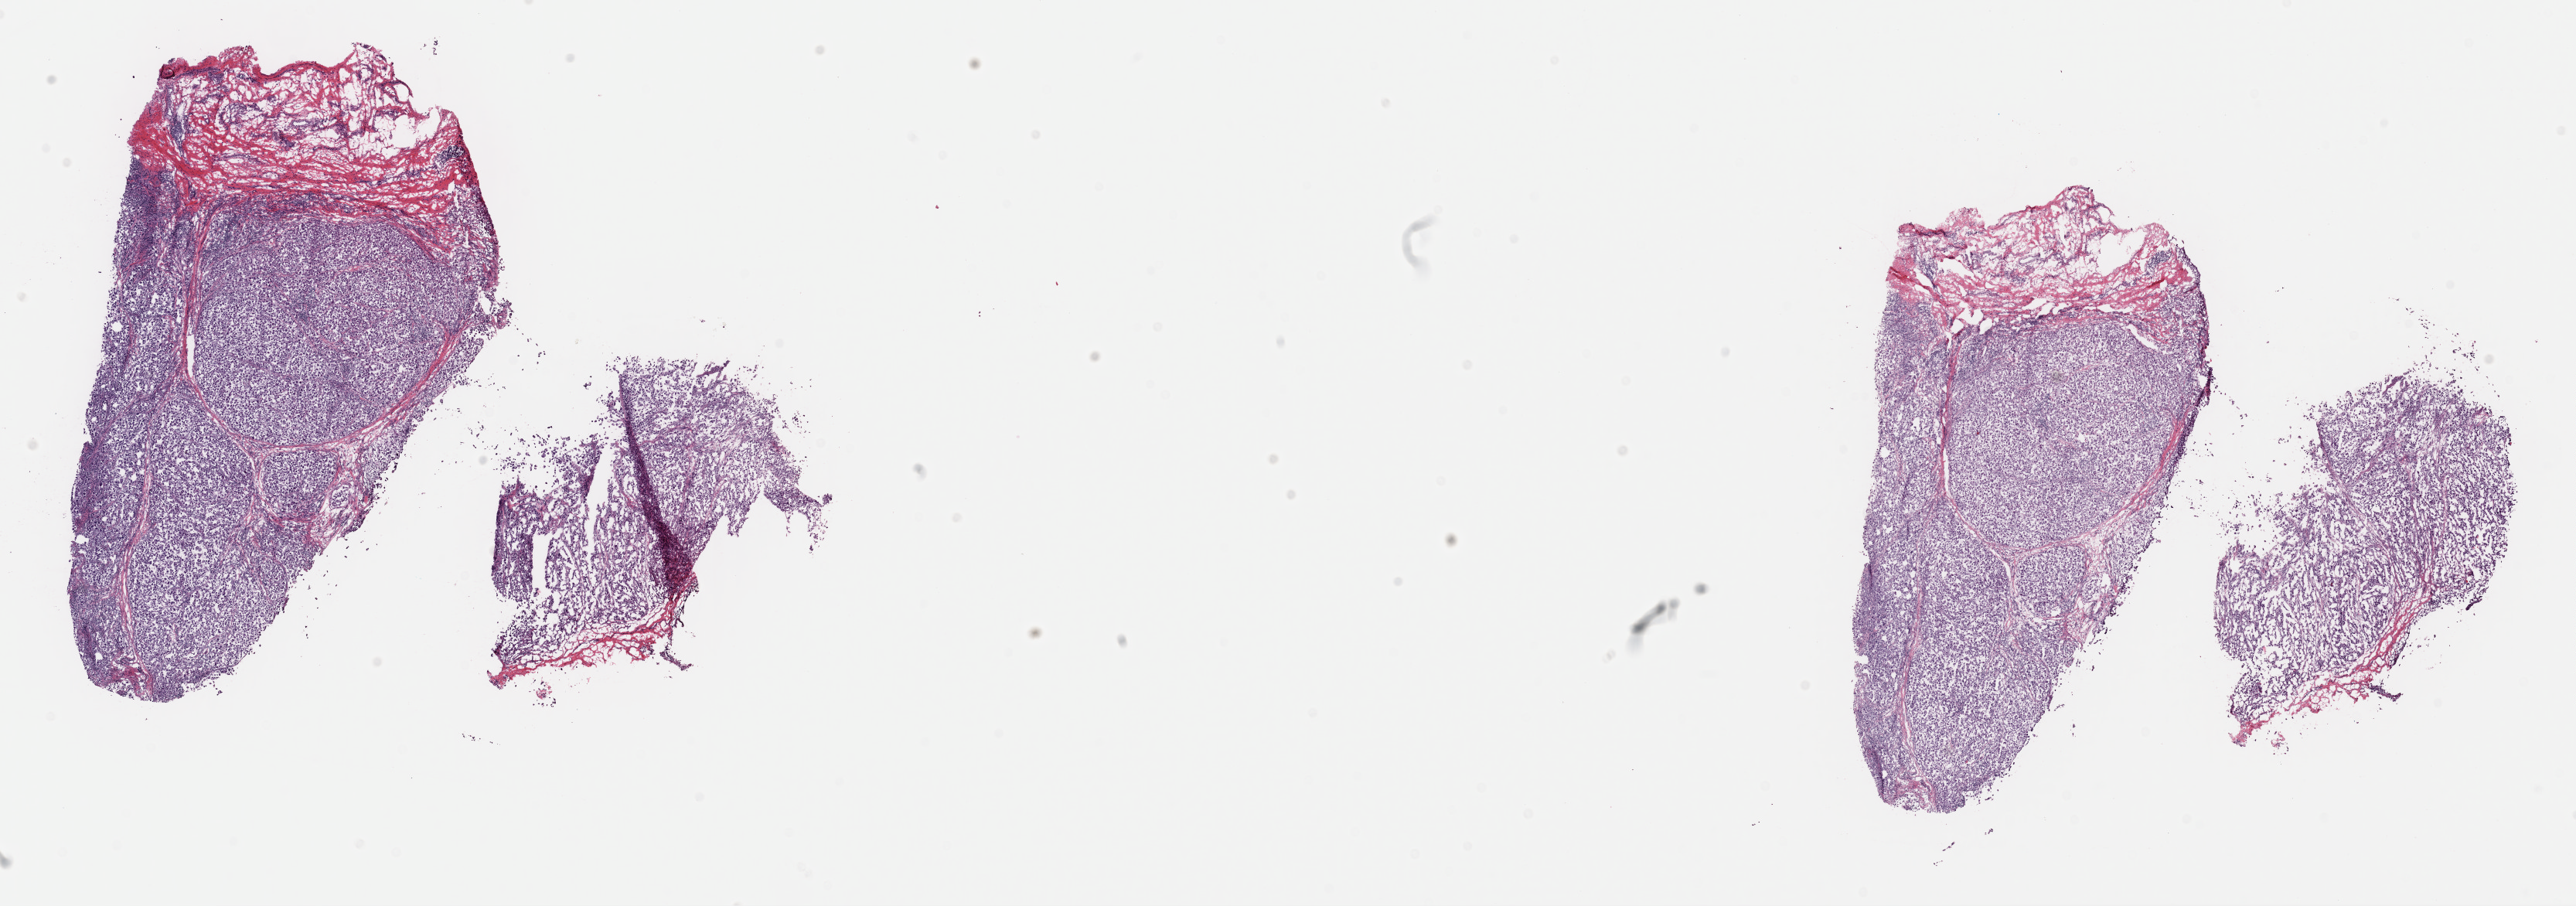
Digitized Hematoxylin and eosin (H&E) stained tissue section (whole slide) — a low-resolution overview of the entire scanned area, about 26.3 x 9.3 mm (slide scanned at 40x). Frozen section from the top of the tissue portion. Metastatic tumour sample. Male, age 67 years at initial diagnosis. Composition of this section per pathologist review: tumour cells 85%, tumour nuclei 85%, normal cells 0%, stromal cells 15%, necrosis 0%. Inflammatory infiltration, as recorded: lymphocyte infiltration 0%, monocyte infiltration 0%, neutrophil infiltration 0%.
This section: metastatic tumour tissue. Patient diagnosis: Malignant melanoma, NOS.